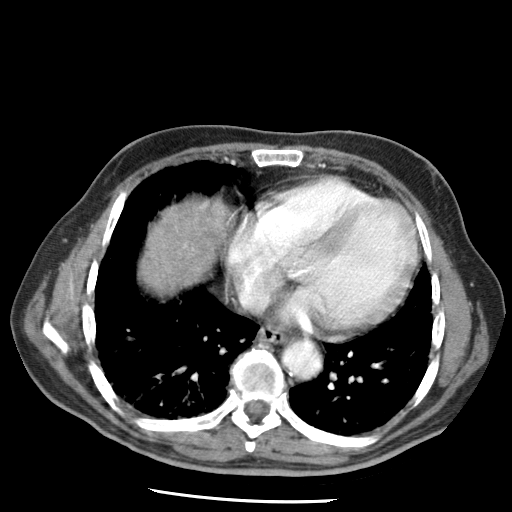
Contrast-enhanced abdominal CT (liver protocol), one axial slice. Slice 67 of 79 in the series (ordered by position). Reconstruction kernel STANDARD. 120 kVp. Soft-tissue window (W 400 / L 40 HU). 2.5 mm slice thickness. 512 × 512 image matrix, field of view 320 × 320 mm. From the clinical record (not read from this slice): diagnosis: hepatocellular carcinoma (patient treated with transarterial chemoembolisation; whether this scan precedes or follows treatment is not stated here); TNM stage (as recorded): Stage-IIIA; Child-Pugh class: A; tumour differentiation: moderately differentiated; tumour nodularity: multinodular.
Structures marked on this image (semi-automatic segmentation, software-assisted and operator-edited):
- liver parenchyma outside the tumour (the mass and vessels are separate outlines, so this box may not span the whole liver): bounding box (x1, y1, x2, y2) in pixels: (140, 200, 234, 292)